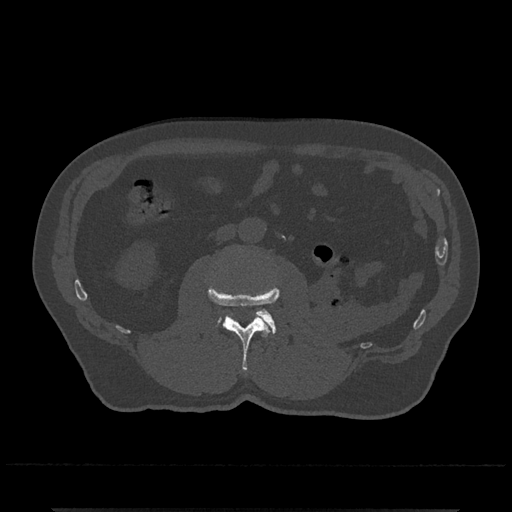
CT including the spine, one axial slice; reconstruction kernel Br40s/3; 120 kVp; bone window (W 1800 / L 400 HU); 512 × 512 image matrix. Male patient, age 67 years. Case-level facts recorded for this patient, not image findings: primary cancer: prostate.
Outlined on this slice (semi-automatically segmented with operator editing):
- L2 vertebra: bounding box (x1, y1, x2, y2) in pixels: (208, 286, 279, 371)
- L3 vertebra: (218, 309, 276, 335)